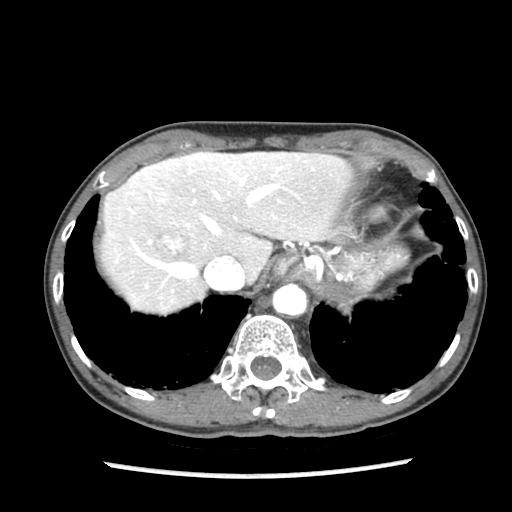
Contrast-enhanced abdominal CT (liver protocol), one axial slice; reconstruction kernel STANDARD; soft-tissue window (W 400 / L 40 HU); 512 × 512 image matrix, field of view 300 × 300 mm. From the clinical record (not read from this slice): diagnosis: hepatocellular carcinoma (patient treated with transarterial chemoembolisation; whether this scan precedes or follows treatment is not stated here); TNM stage (as recorded): Stage-IIIB; Child-Pugh class: A; tumour differentiation: well differentiated; tumour nodularity: uninodular.
Structures marked on this image (semi-automatic segmentation, software-assisted and operator-edited):
- liver parenchyma outside the tumour (the mass and vessels are separate outlines, so this box may not span the whole liver): bounding box [x1, y1, x2, y2] px = [100, 152, 352, 314]
- mass: [154, 228, 188, 258]
- liver vessels: [128, 157, 282, 292]